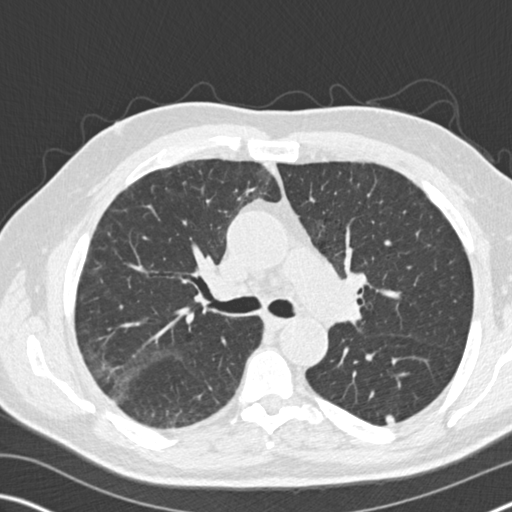
Low-dose screening chest CT, one axial slice. Position 107 of 169 along the scan axis. Reconstruction kernel B30f. Lung window (W 1500 / L -600 HU). 2 mm slice thickness. 512 × 512 image matrix, field of view 340 × 340 mm.
Annotated regions visible in this slice (expert manual segmentation):
- lesion 2 (nodule, lower lobe of left lung): bounding box [x1, y1, x2, y2] px = [386, 415, 395, 425]